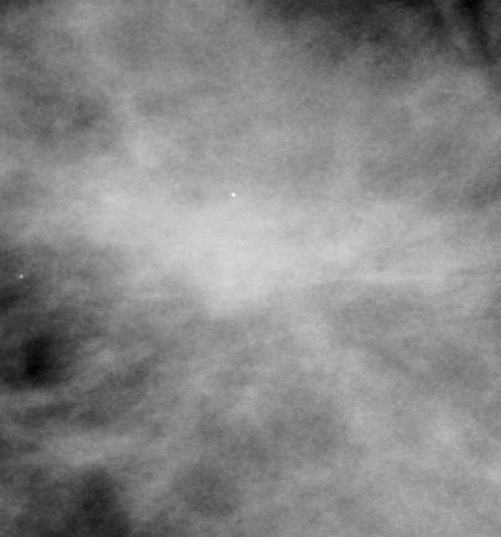
Region of interest cut from a scanned film mammogram (one marked finding), left breast, CC view, BI-RADS breast density category 3 (scale 1–4).
- Finding: mass, shape architectural distortion; BI-RADS assessment category 0 (incomplete: needs additional imaging); subtlety rating 5 on a 1 (subtle) to 5 (obvious) scale; pathology result (as recorded, not read from the image): malignant.